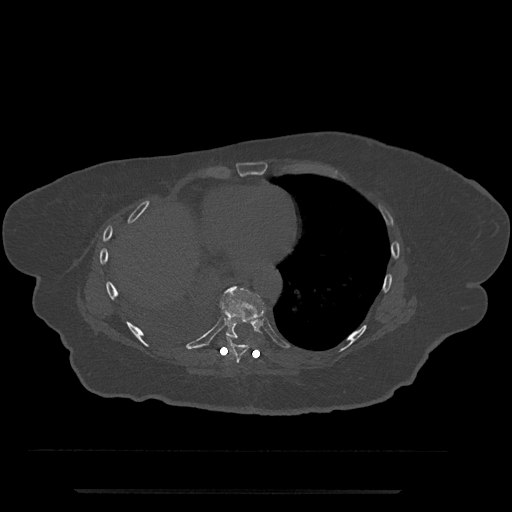
CT including the spine, one axial slice. Position 366 of 797 along the scan axis. 120 kVp. Bone window (W 1800 / L 400 HU). 0.5 mm slice thickness. 512 × 512 image matrix, field of view 440 × 440 mm. Patient: female, 51 years. From the clinical record (not read from this slice): primary cancer: neuro; vertebrae with lytic lesions (as recorded): T8.
Outlined on this slice (semi-automatically segmented with operator editing):
- T8 vertebra: bounding box [x1, y1, x2, y2] px = [226, 337, 249, 363]
- T9 vertebra: [219, 286, 266, 340]